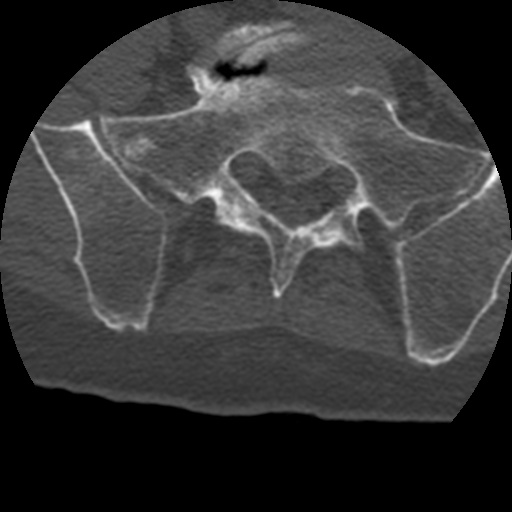
CT including the spine, one axial slice. Position 25 of 399 along the scan axis. Reconstruction kernel STANDARD. 120 kVp. Bone window (W 1800 / L 400 HU). 1.25 mm slice thickness. 512 × 512 image matrix, field of view 160 × 160 mm. Patient age 69 years. Case-level facts recorded for this patient, not image findings: primary cancer: prostate.
Annotated regions visible in this slice (semi-automatically segmented with operator editing):
- L5 vertebra: bounding box (x1, y1, x2, y2) in pixels: (210, 20, 318, 65)